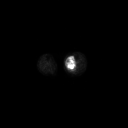
FDG PET of an extremity soft-tissue mass (from a PET/CT study), one axial slice. Position 141 of 223 along the scan axis. 128 × 128 image matrix, field of view 700 × 700 mm. Female patient, age 70 years. Case-level facts recorded for this patient, not image findings: histological type: extraskeletal high grade osteogenic sarcoma; grade: high; site of the primary tumour: left calf.
Structures marked on this image (expert contour drawn on MRI and transferred to this co-registered scan by the dataset authors):
- gross tumour volume (mass): bounding box (x1, y1, x2, y2) in pixels: (66, 58, 76, 70)